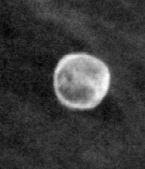
Region of interest cut from a scanned film mammogram (one marked finding); left breast; MLO view.
Calcifications, morphology lucent center; BI-RADS assessment category 2; subtlety rating 5 on a 1 (subtle) to 5 (obvious) scale; benign without callback (not worked up further).